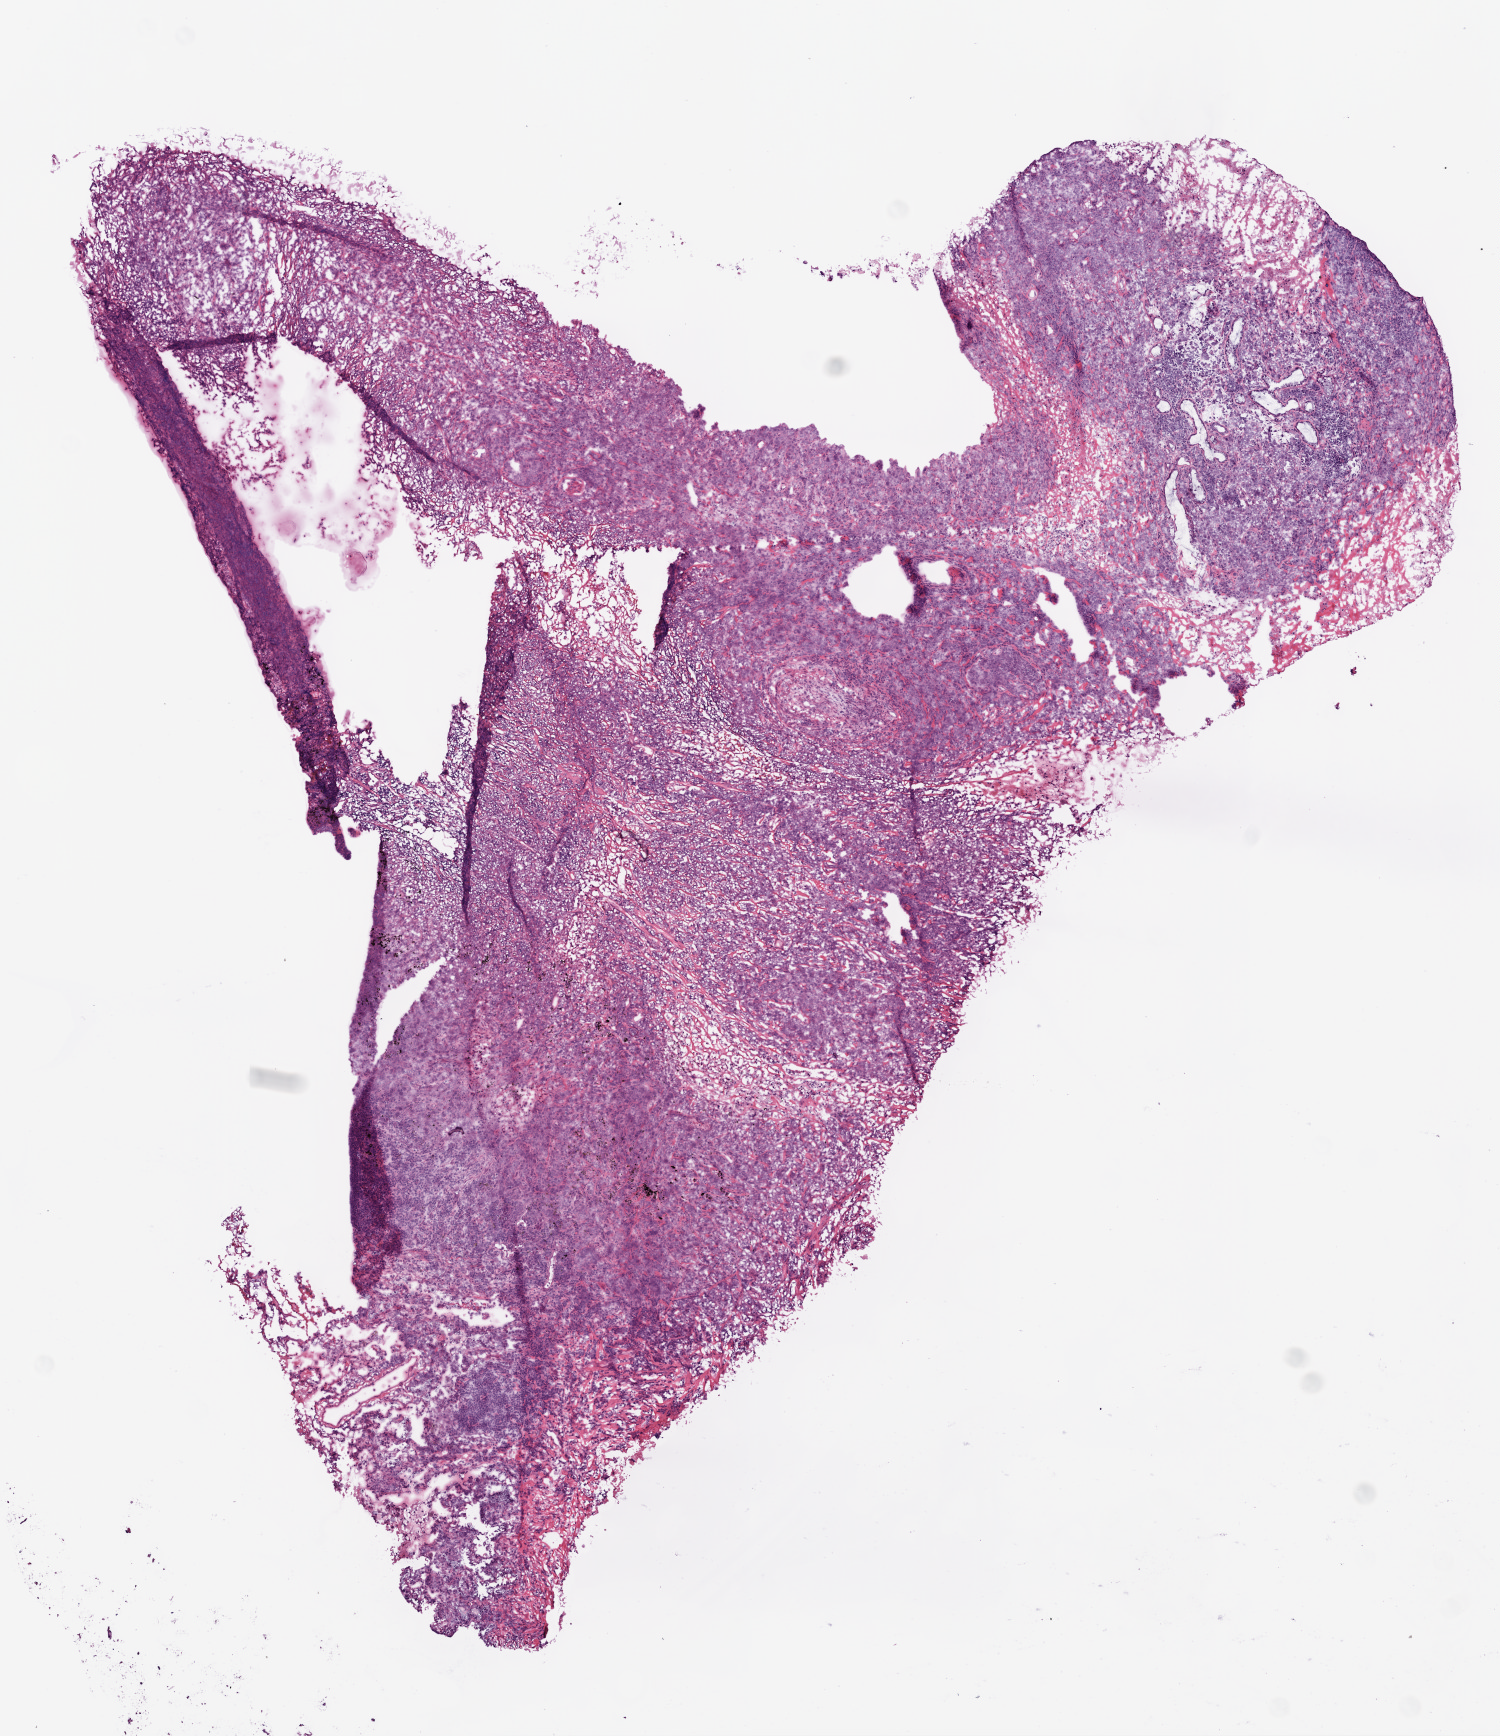
Whole-slide histology image, H&E, whole scanned area (about 6.0 x 7.0 mm, from a 20x scan) shown as a low-resolution overview, frozen section from the bottom of the tissue portion, lung, primary tumour sample. Male patient; age at initial diagnosis 71 years. Slide review estimates, as recorded: tumour cells 80%, tumour nuclei 90%, normal cells 0%, stromal cells 5%, necrosis 15%. Infiltration values recorded for this section: lymphocyte infiltration 5%, neutrophil infiltration 1%.
Histologic diagnosis: Squamous cell carcinoma, NOS (lower lobe, lung). TNM: T2 N1 M0. AJCC pathologic stage: IIB.